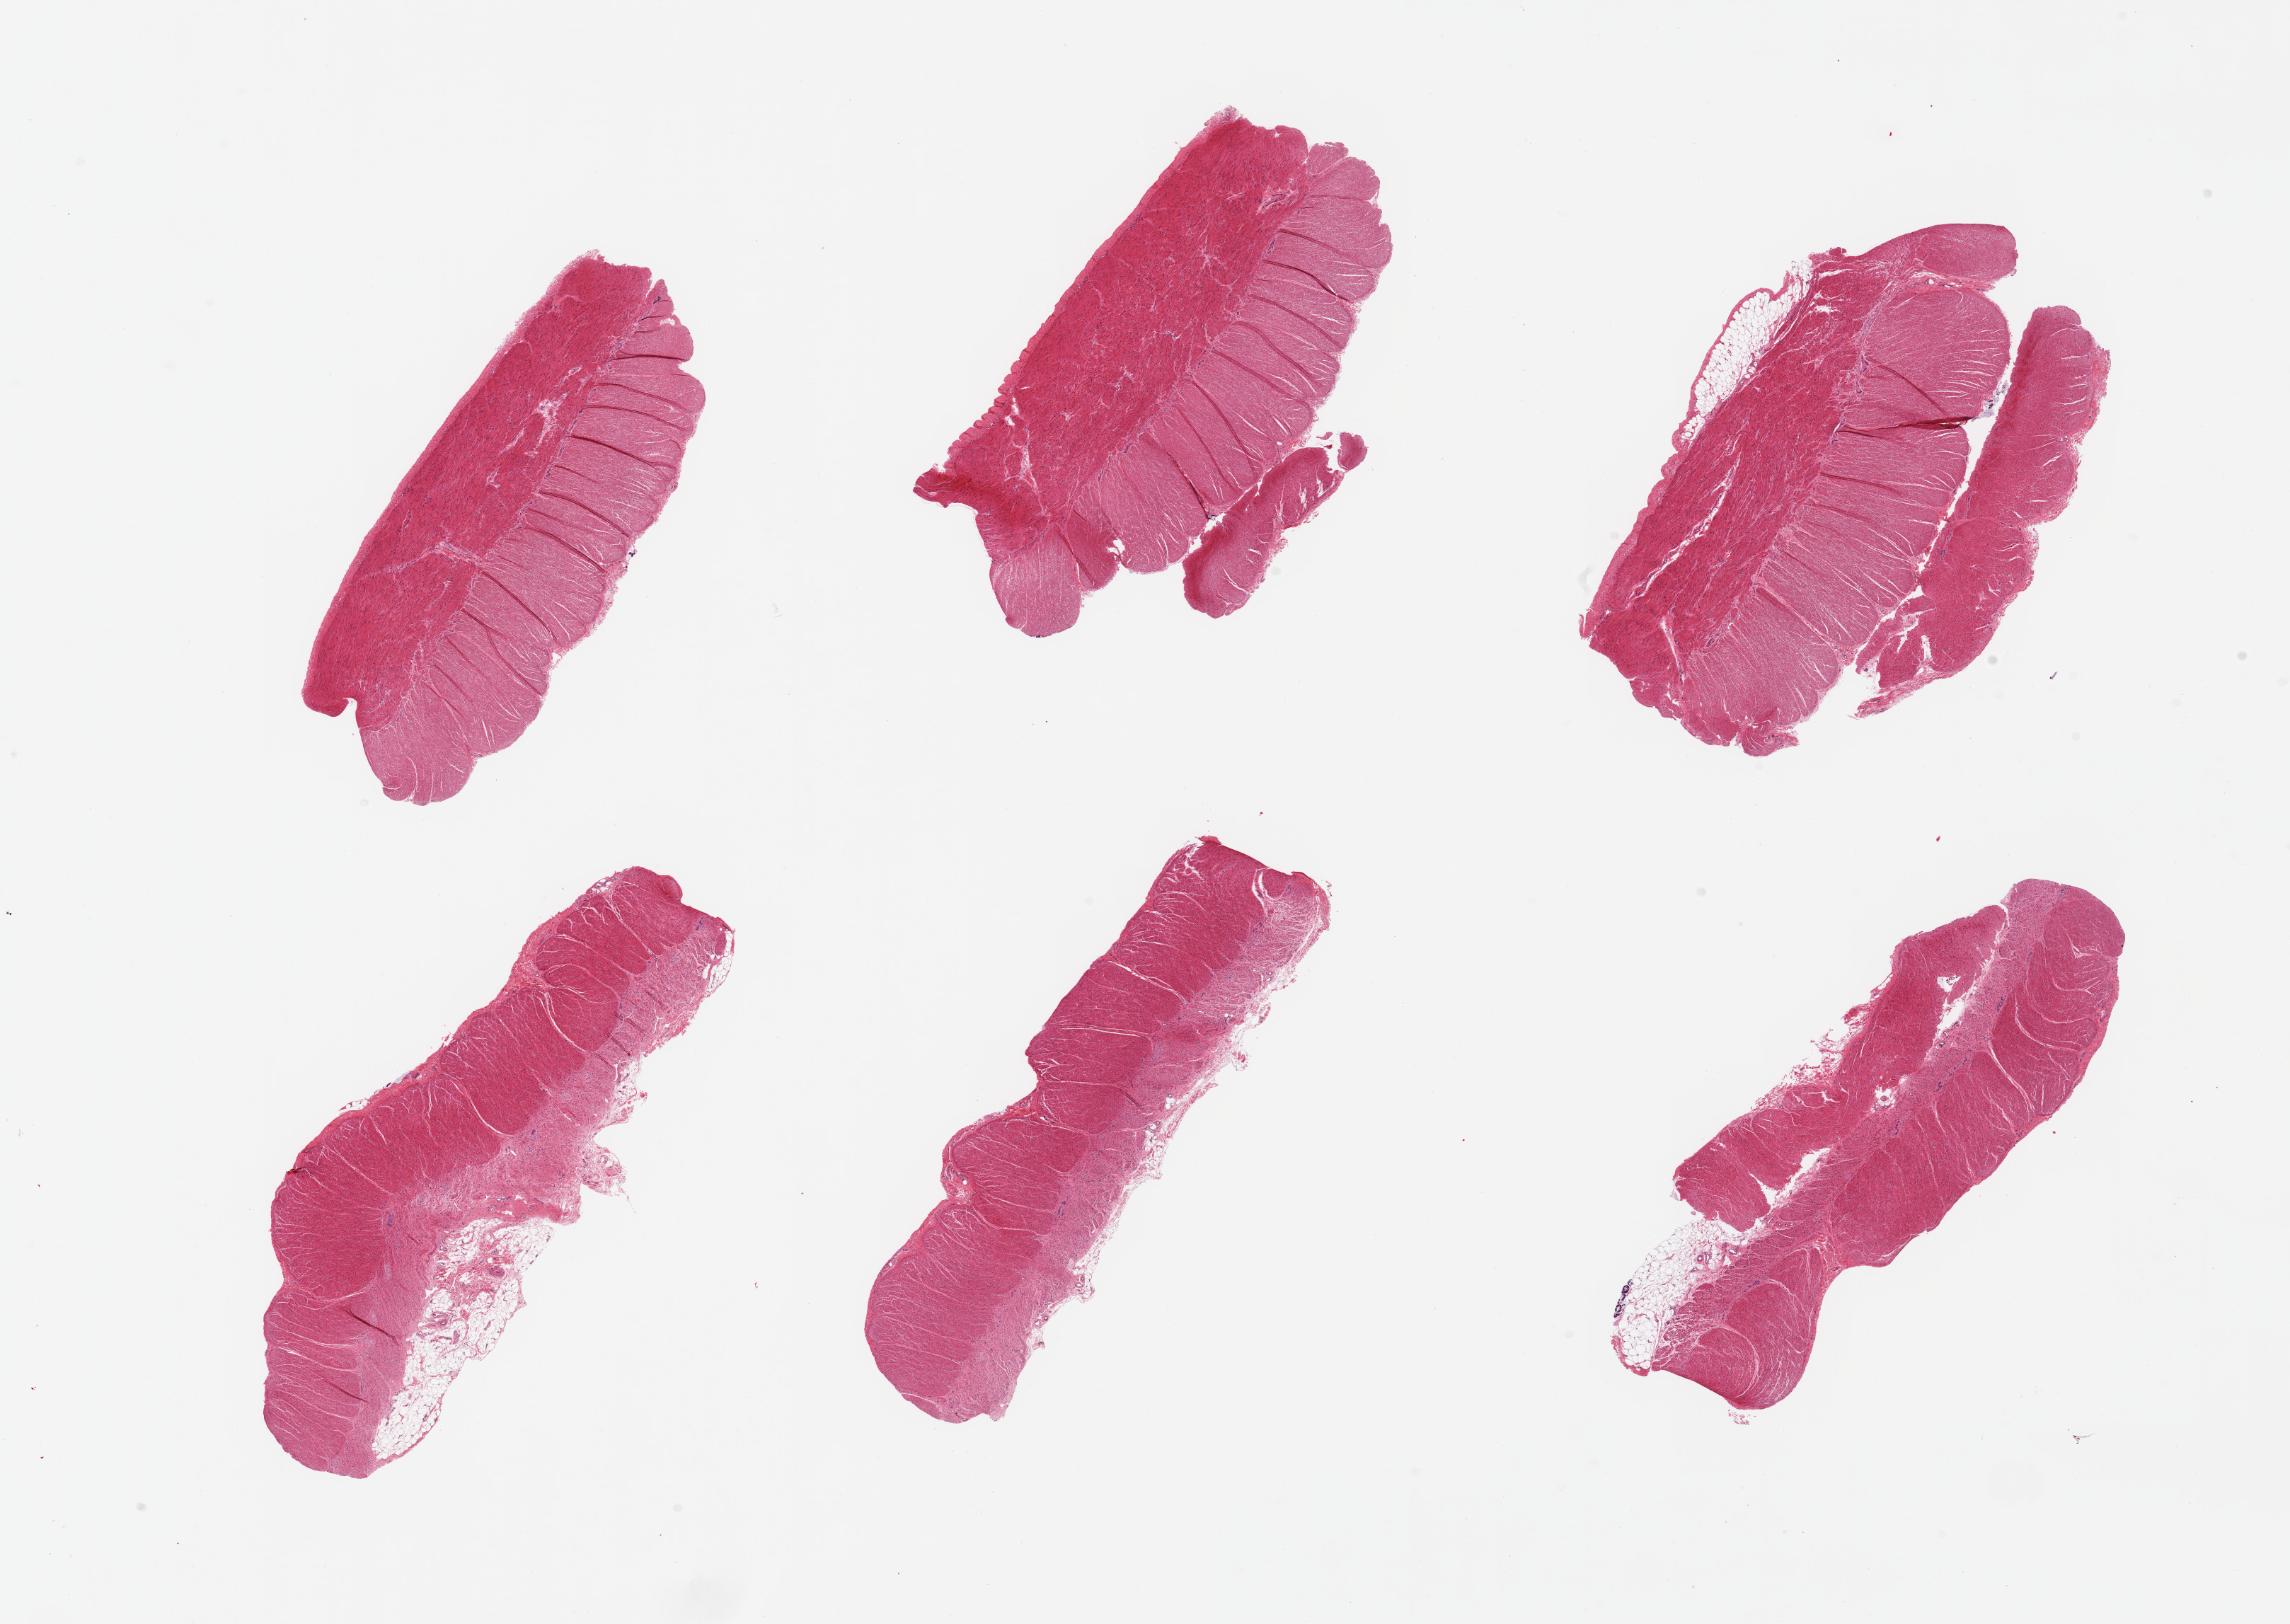
Digitized hematoxylin and eosin (H&E)-stained section, brightfield, whole scanned area (about 25.6 x 18.2 mm, acquisition: 20x scan) shown as a low-resolution overview; PAXgene-fixed, paraffin-embedded tissue; target tissue: sigmoid colon; donor tissue sample.
Review note (as recorded): 6 pieces, confirmed target muscularis.